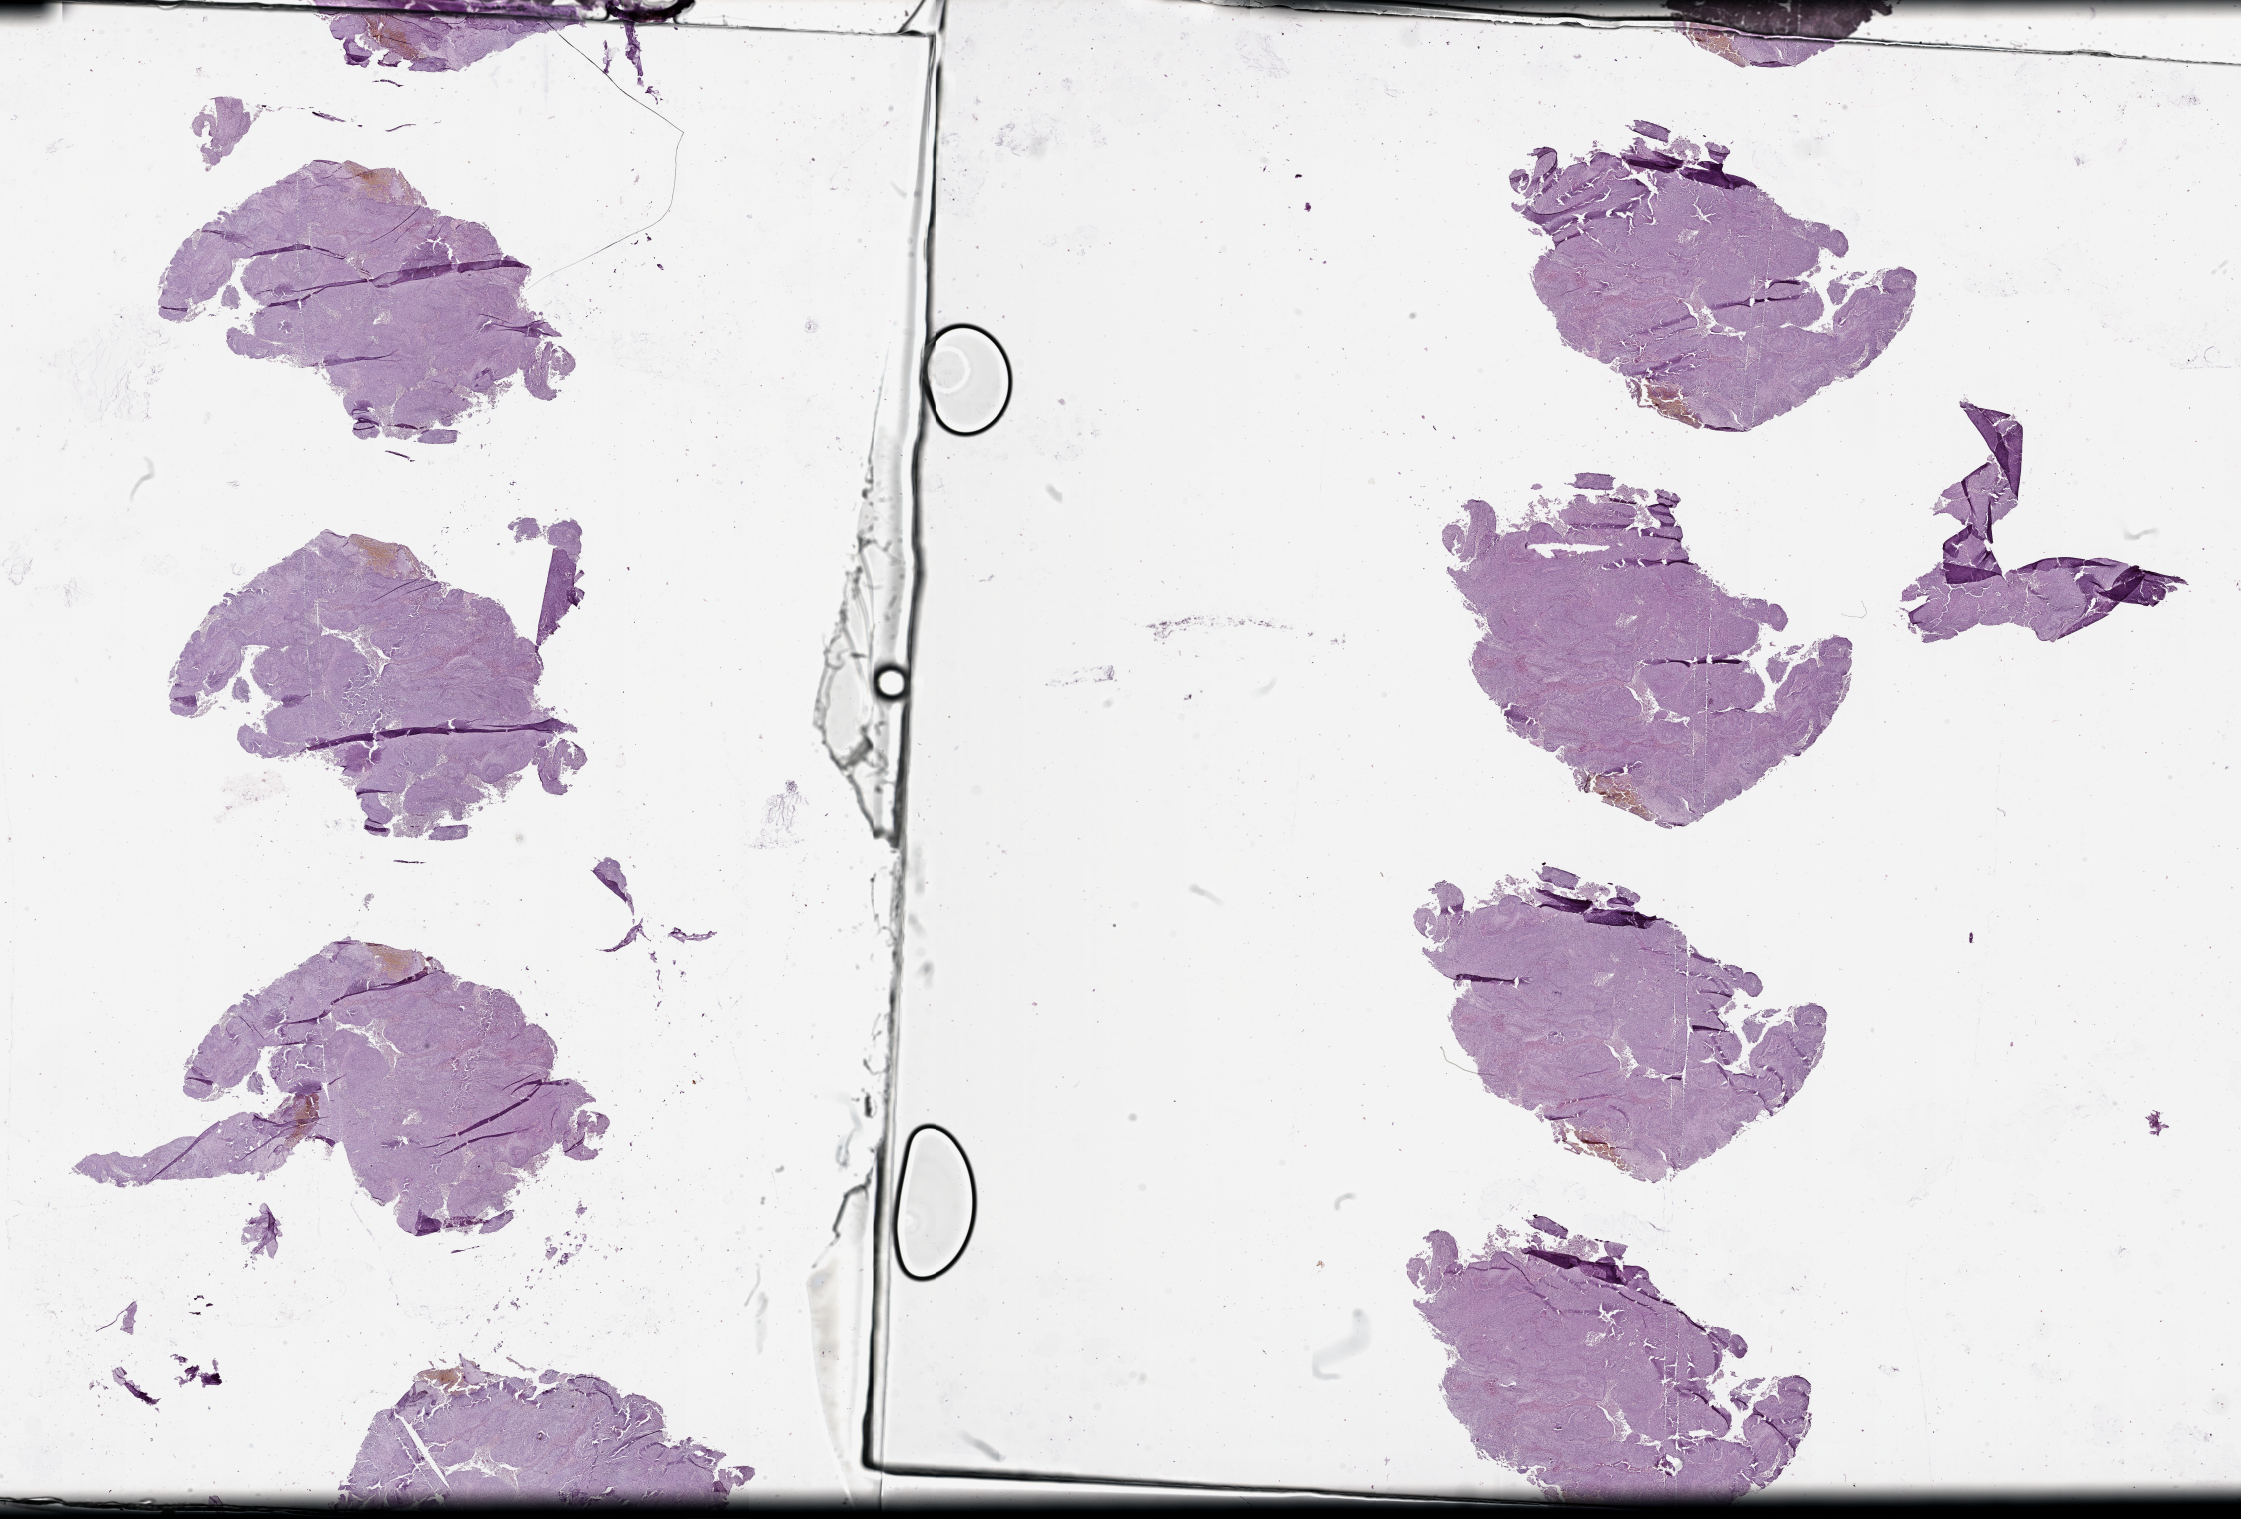
Whole-slide histology image, Hematoxylin and eosin (H&E) stained — shown as a low-resolution overview of the whole scanned area (about 36.1 x 24.5 mm); lung, tumour tissue. Patient: female, age 63 years.
Patient diagnosis (cohort enrolment): squamous cell carcinoma (lung).